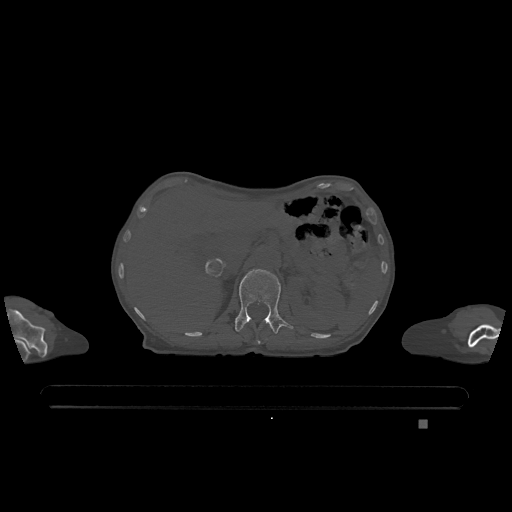
CT including the spine, one axial slice; position 485 of 1317 along the scan axis; bone window (W 1800 / L 400 HU); 0.5 mm slice thickness; 512 × 512 image matrix, field of view 500 × 500 mm. Female patient, age 74 years. From the clinical record (not read from this slice): primary cancer: lung; vertebrae with lytic lesions (as recorded): T1, T4, T5, T6, L4, L5.
Outlined on this slice (semi-automatic segmentation, software-assisted and operator-edited):
- L1 vertebra: bounding box [x1, y1, x2, y2] px = [235, 269, 293, 334]
- T12 vertebra: [257, 340, 261, 344]